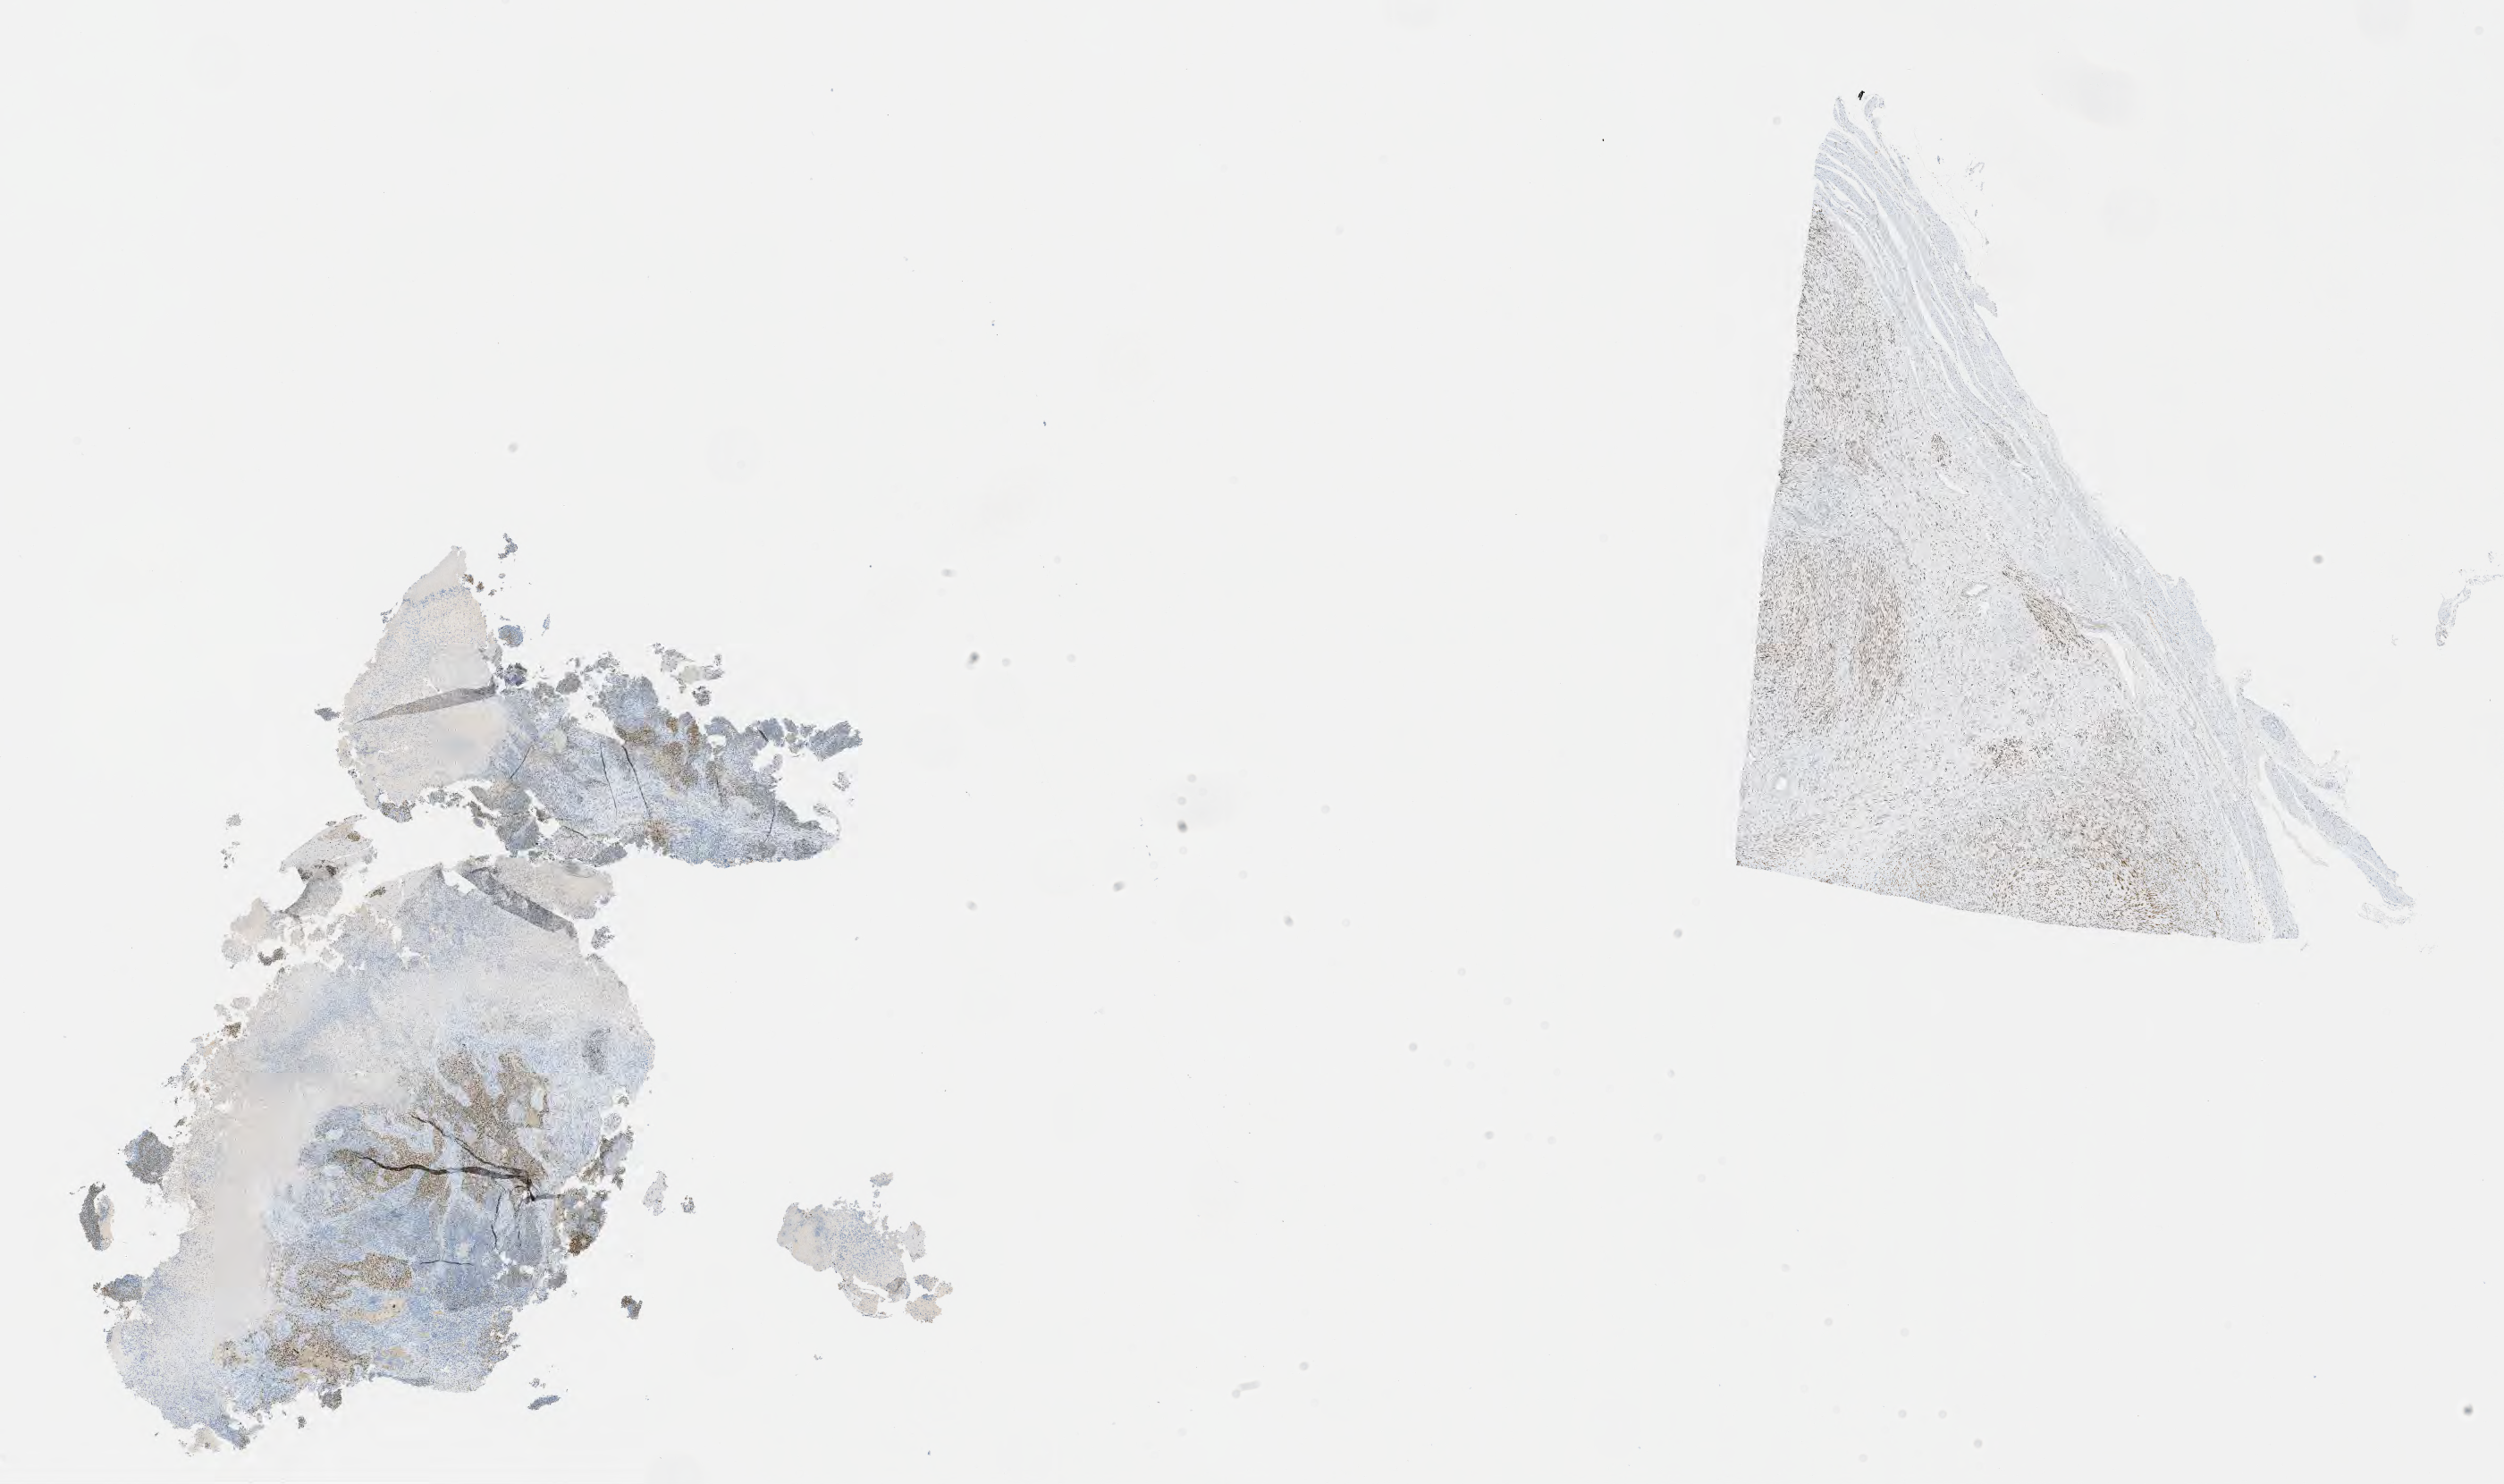
Whole-slide image, immunohistochemical stain for estrogen receptor (ER), a low-resolution overview of the entire scanned area, about 22.6 x 13.4 mm. Specimen: tumor tissue. Anatomic site: cervix. Female patient, aged 65.
• histologic diagnosis: Squamous cell carcinoma, large cell, nonkeratinizing, NOS